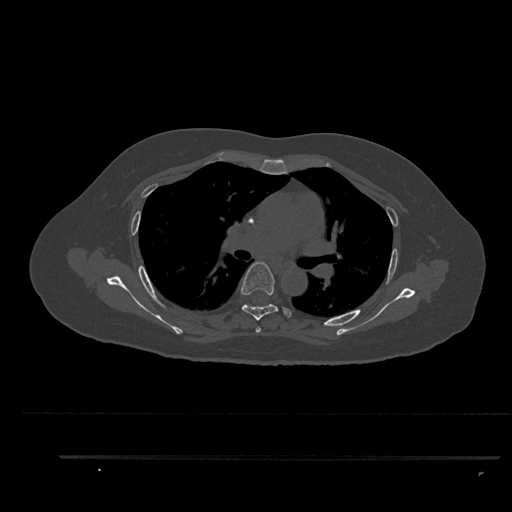
CT including the spine, one axial slice; slice 600 of 797 in the series (ordered by position); reconstruction kernel Br40s/3; 120 kVp; bone window (W 1800 / L 400 HU); 512 × 512 image matrix, field of view 408 × 408 mm. Female patient, age 44 years. Case-level facts recorded for this patient, not image findings: primary cancer: renal; vertebrae with lytic lesions (as recorded): L1.
Outlined on this slice (semi-automatic segmentation, software-assisted and operator-edited):
- T4 vertebra: bounding box (x1, y1, x2, y2) in pixels: (256, 326, 261, 333)
- T5 vertebra: (241, 262, 292, 320)
- T6 vertebra: (263, 304, 269, 307)